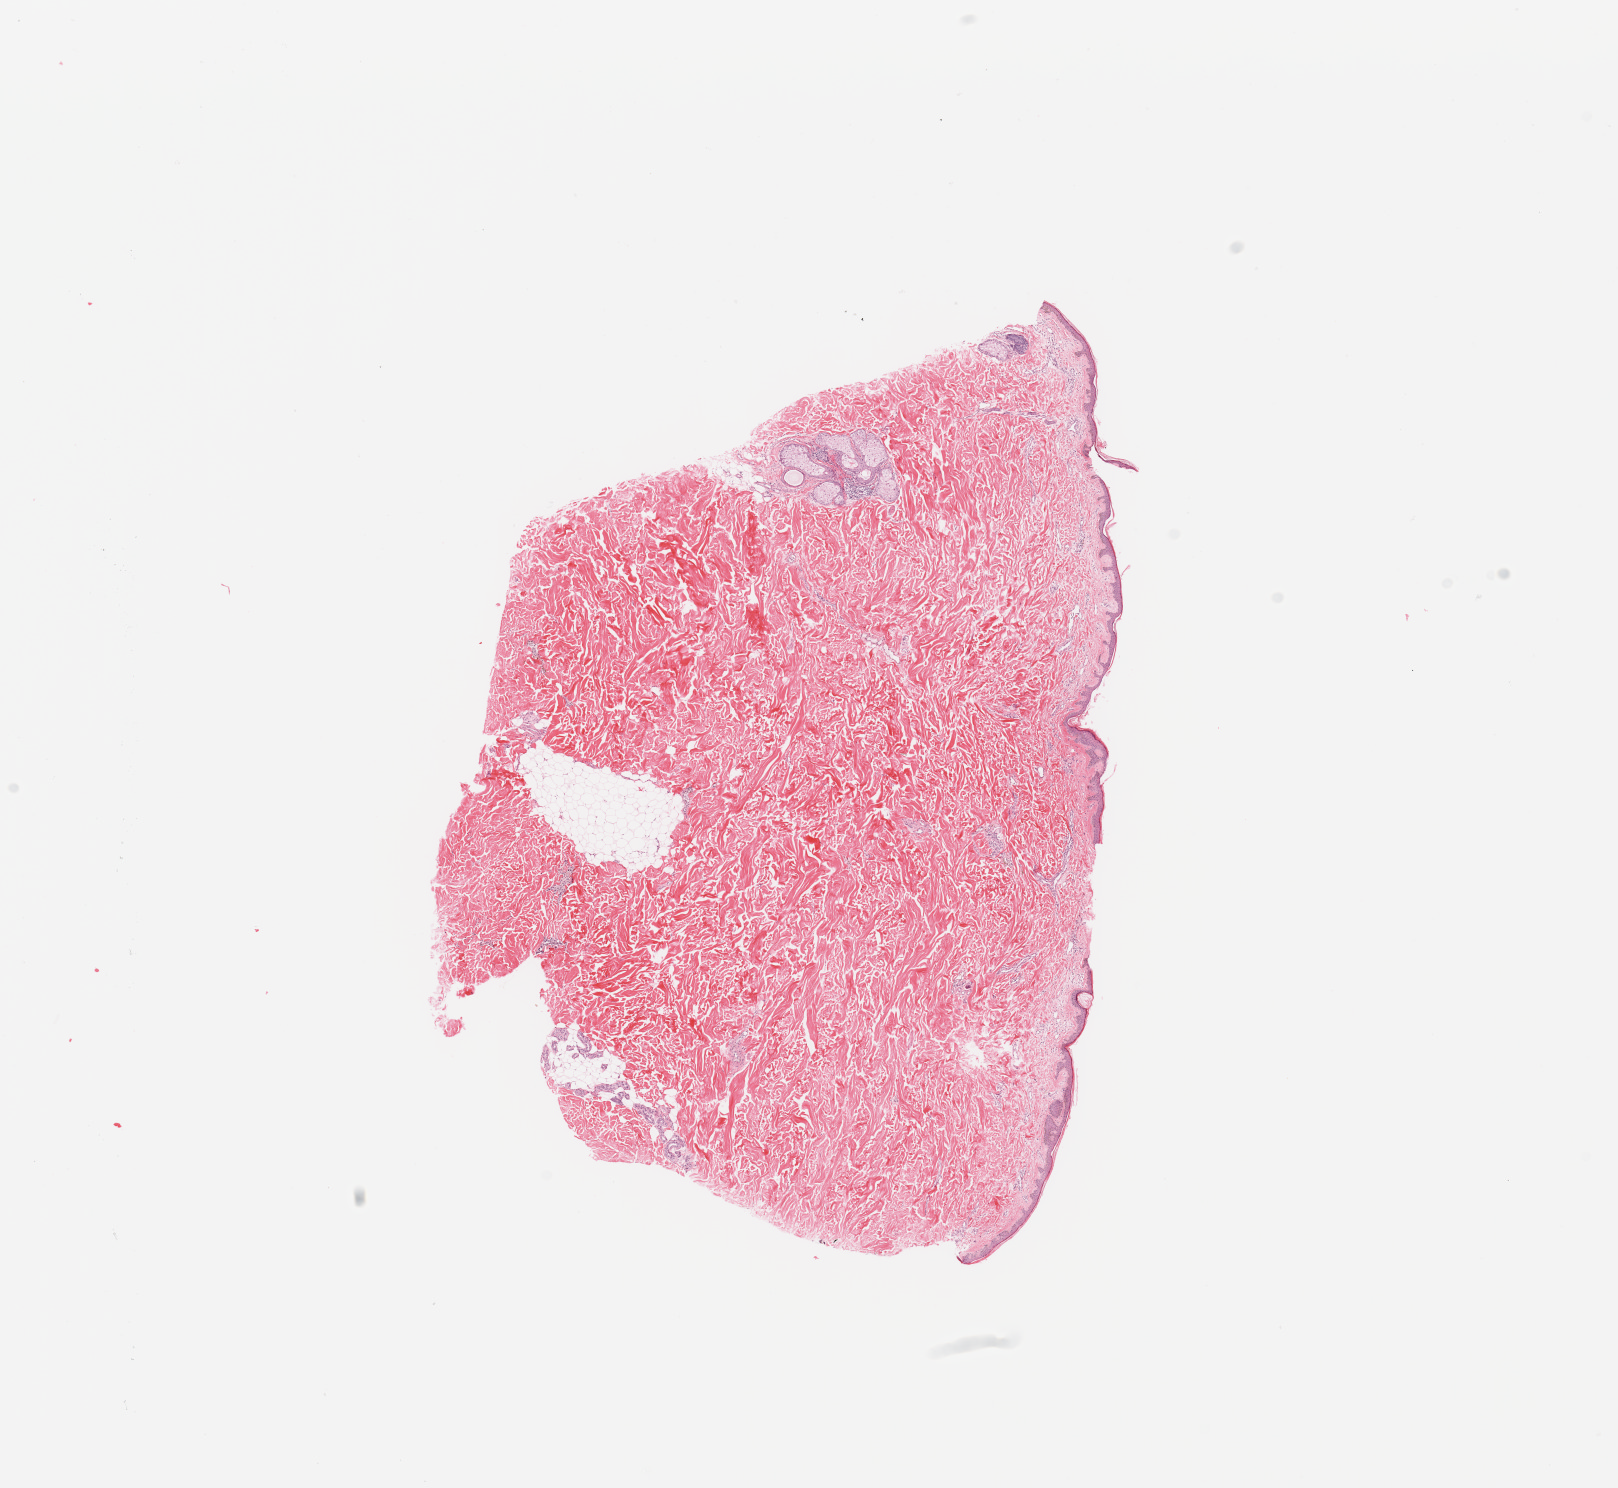
Hematoxylin and eosin (H&E) stained whole-slide image — low-resolution overview of the scanned area, about 12.8 x 11.8 mm (from a 20x scan). Normal (non-tumour) tissue sample, sampled site: trunk. Female, 81 y/o.
- this section: normal (non-tumour) tissue from the same patient
- patient diagnosis: Malignant melanoma, NOS